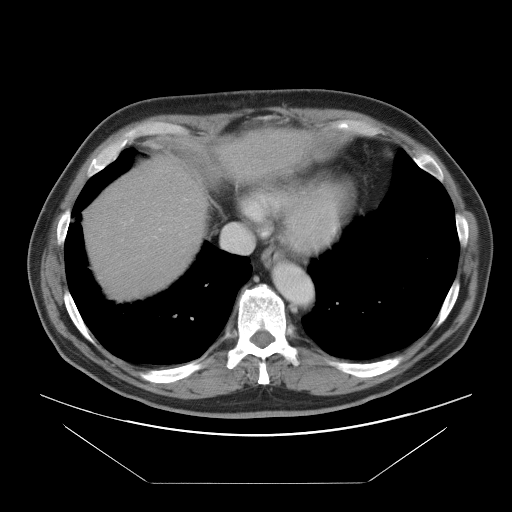
Contrast-enhanced abdominal CT, one axial slice. Slice 84 of 97 in the series (ordered by position). 120 kVp. Intravenous contrast given. Soft-tissue window (W 400 / L 40 HU). 5 mm slice thickness. 512 × 512 image matrix. Male patient, age 62 years. Case-level facts recorded for this patient, not image findings: diagnosis: colorectal cancer liver metastases, imaged before liver resection; multiple liver metastases: no; largest metastasis: 7 cm; disease in both lobes: yes.
Structures marked on this image (expert manual segmentation):
- hepatic veins: box from (x=221, y=204) to (x=260, y=254) px
- liver: (x=86, y=134)–(x=301, y=297)
- planned liver remnant (the part of the liver to remain after resection): (x=86, y=181)–(x=204, y=298)